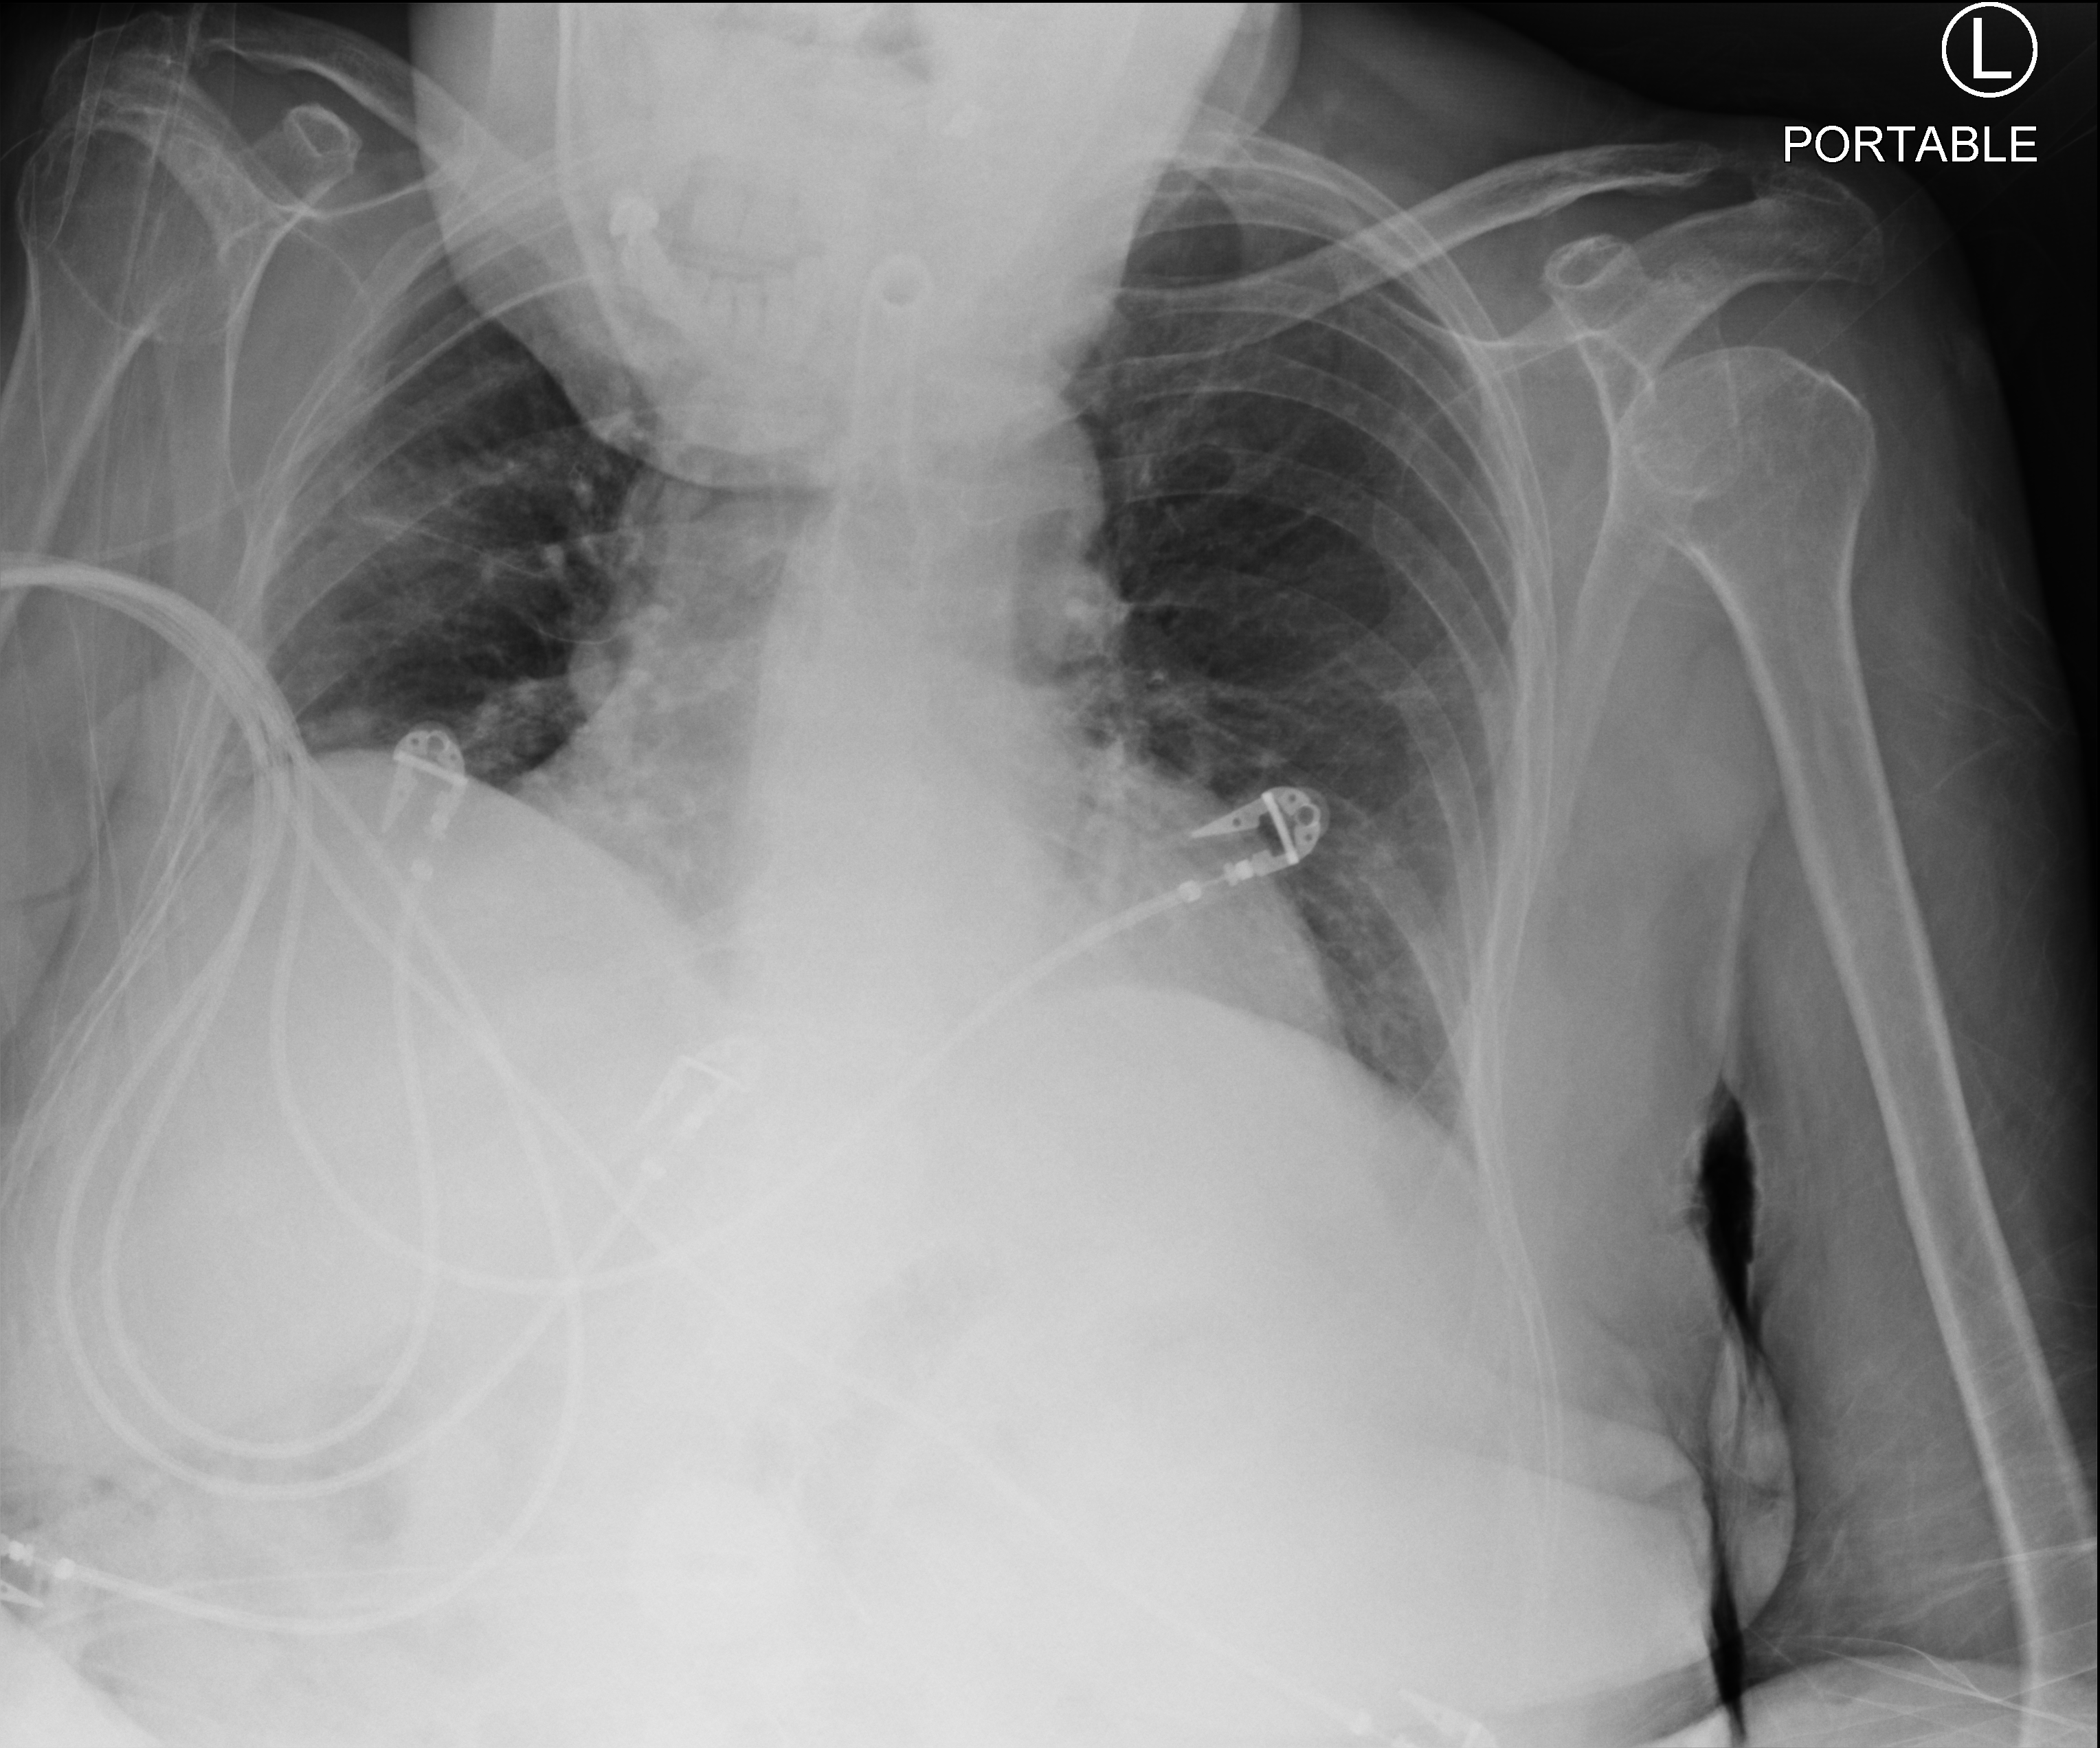
Portable chest radiograph, anteroposterior (AP) projection. Female patient hospitalised with COVID-19, age 75–90 years.
Hospital-stay facts (about this admission, not read from this image; timing relative to this image not recorded):
- admitted to intensive care during this hospital stay: yes
- mechanically ventilated during this hospital stay: yes